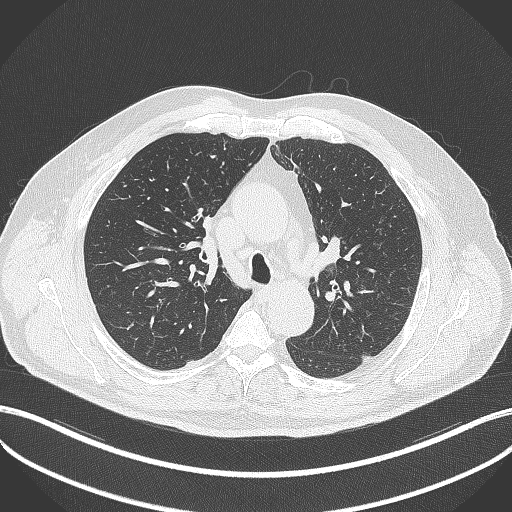
Chest CT, one axial slice. Slice 257 of 411 in the series (ordered by position). Reconstruction kernel B70f. 120 kVp. Lung window (W 1500 / L -600 HU). 512 × 512 image matrix, field of view 400 × 400 mm. Patient: male, 60 years. Case-level facts recorded for this patient, not image findings: clinical TNM (as recorded): T1b N1 M0.
Structures marked on this image (bounding box drawn by a radiologist):
- lung tumour (recorded histology: squamous cell carcinoma): bounding box (x1, y1, x2, y2) in pixels: (200, 214, 219, 237)